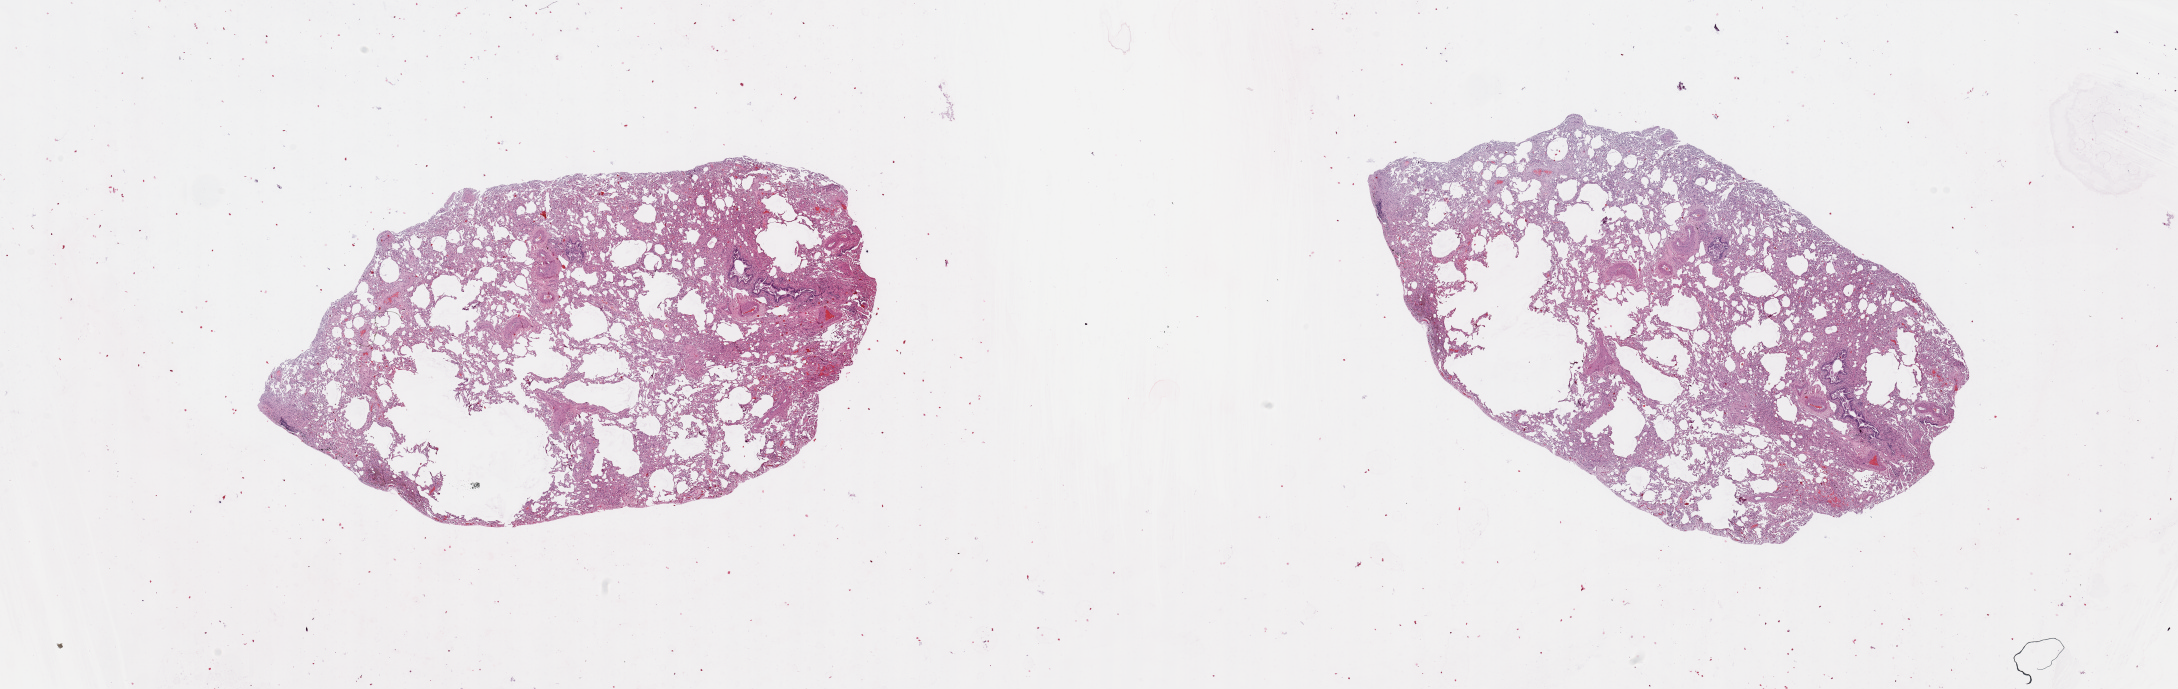
Hematoxylin and eosin (H&E) stained whole-slide image — low-resolution overview of the scanned area, about 34.5 x 10.9 mm; normal (non-tumour) tissue sample, lung. Patient: female, age 64 years.
This section: normal (non-tumour) tissue from the same patient. Patient diagnosis: Squamous cell carcinoma, NOS.